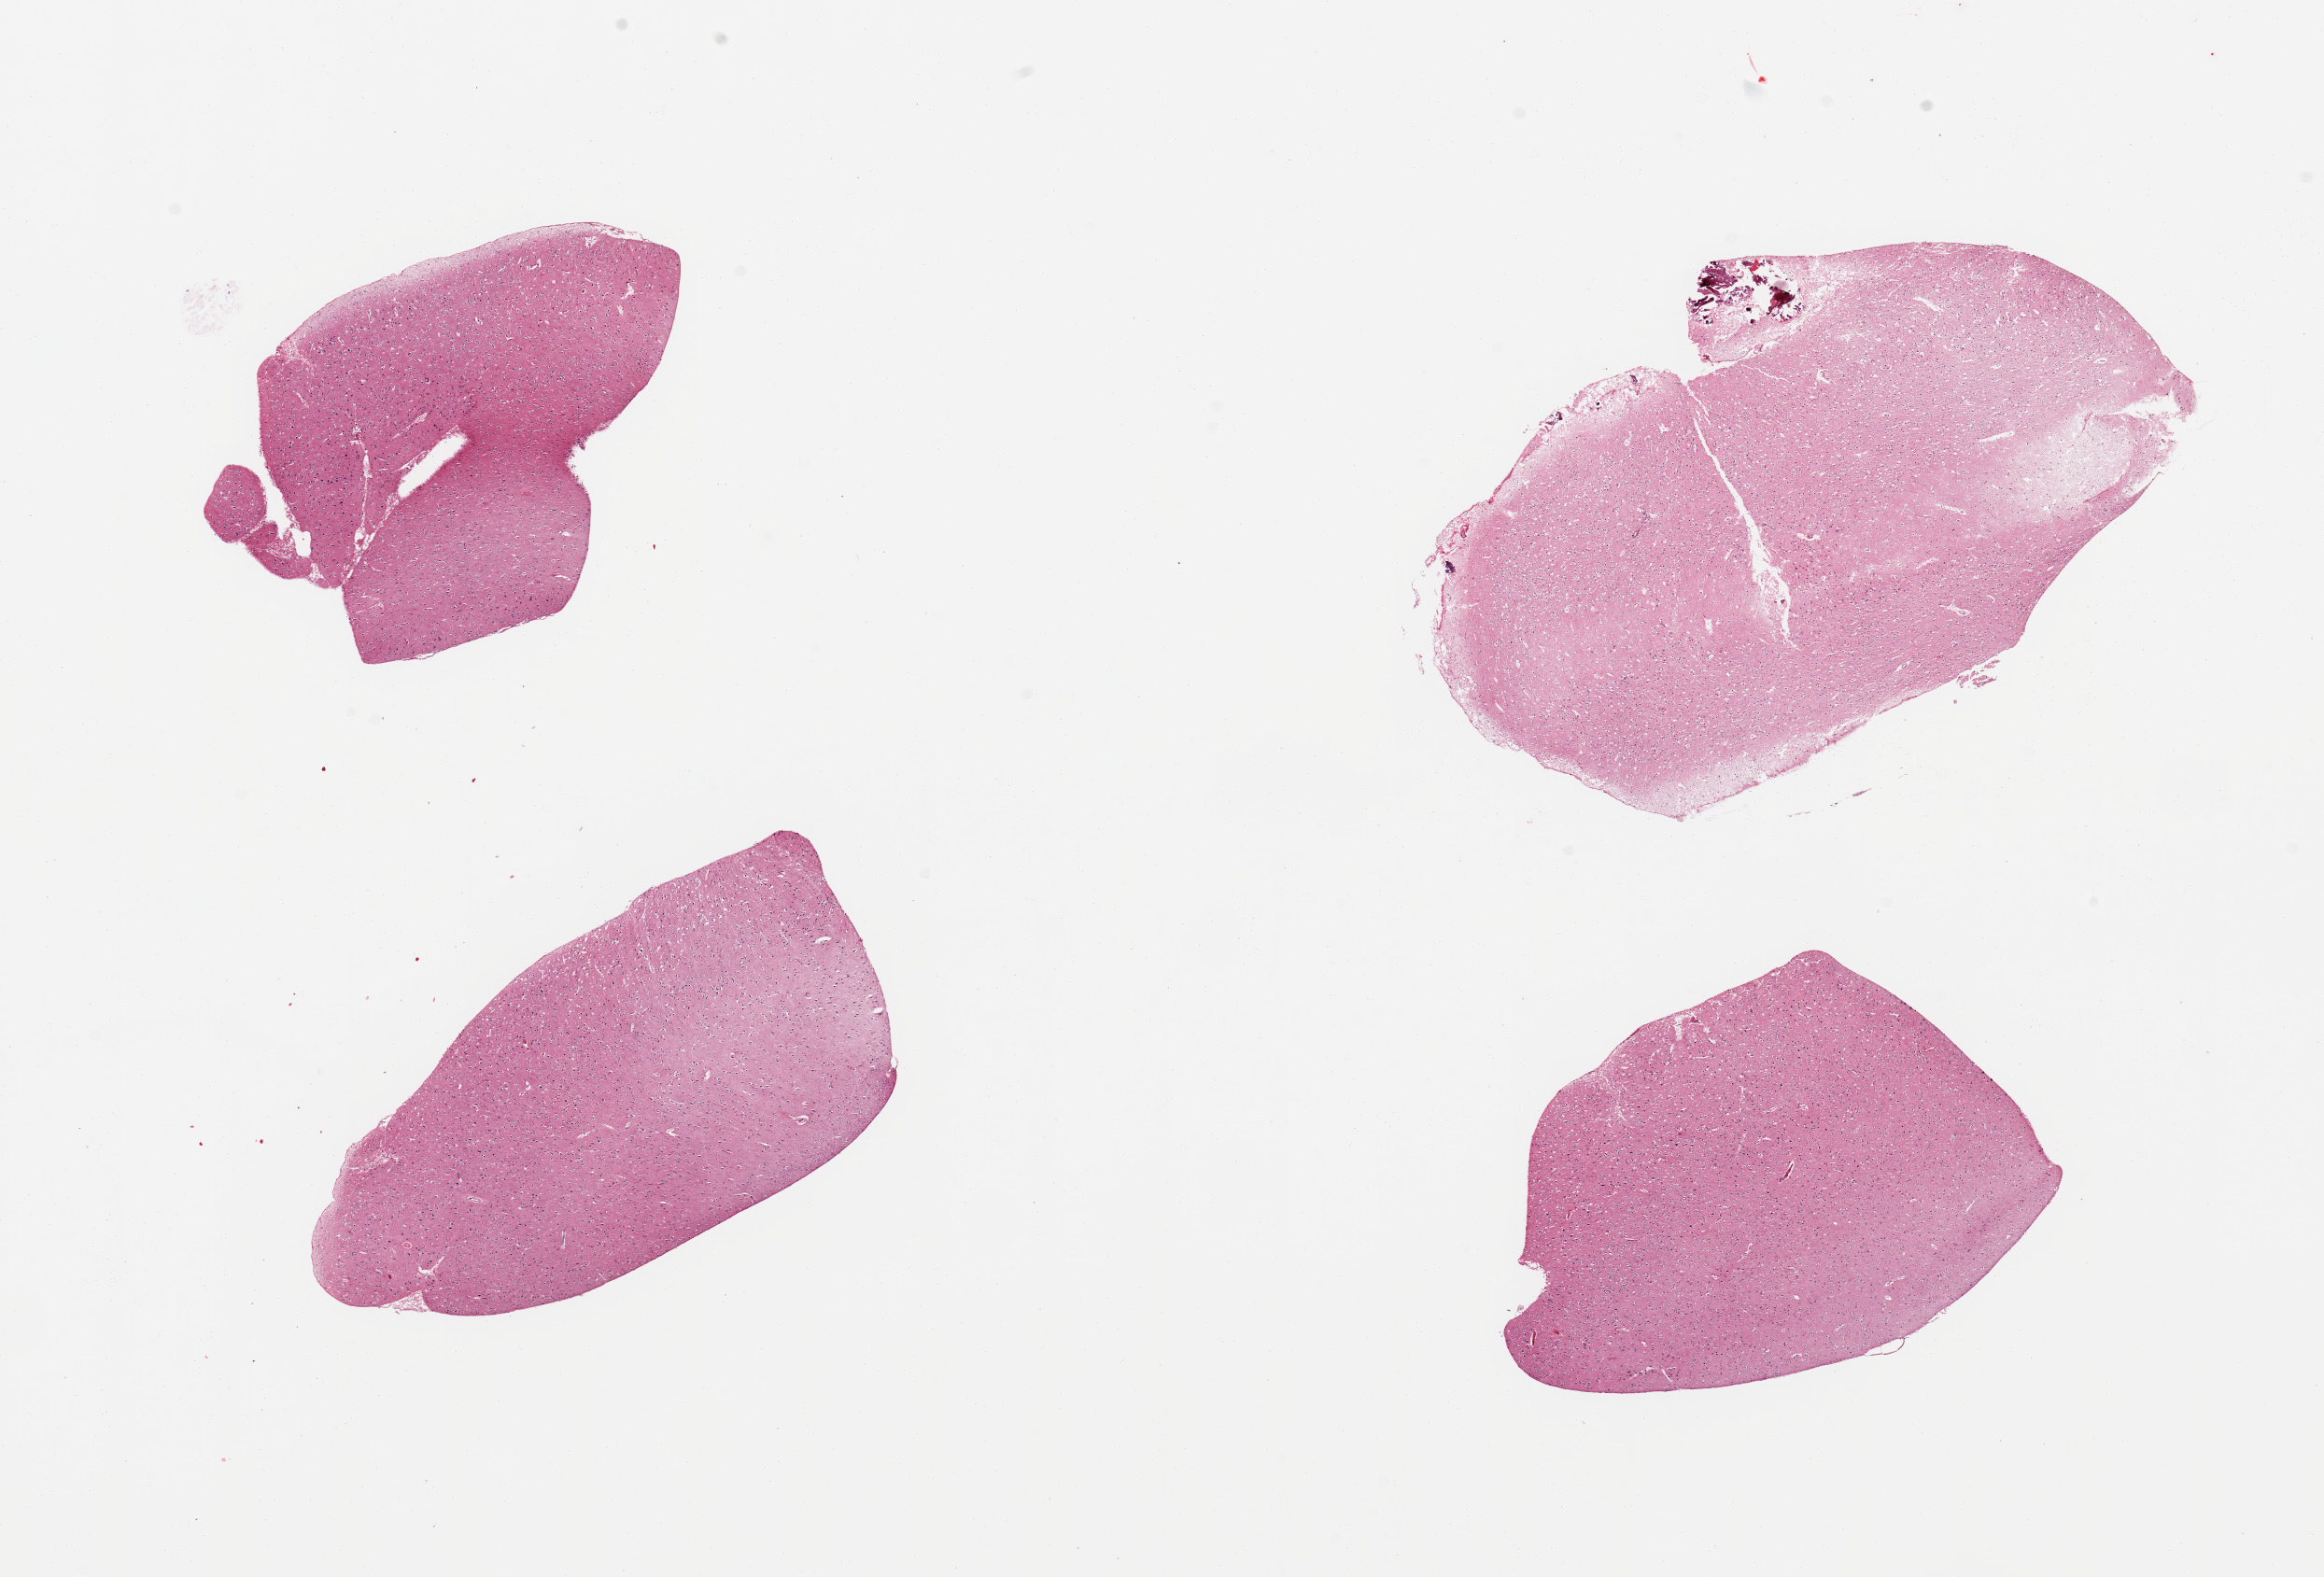
Haematoxylin and eosin whole-slide image, low-resolution overview of the scanned area, about 19.7 x 13.4 mm, PAXgene-fixed, paraffin-embedded tissue, target tissue: cerebral cortex, donor tissue sample. Donor: male.
* pathologist's review note for this sample: 2 pieces, no abnormalities